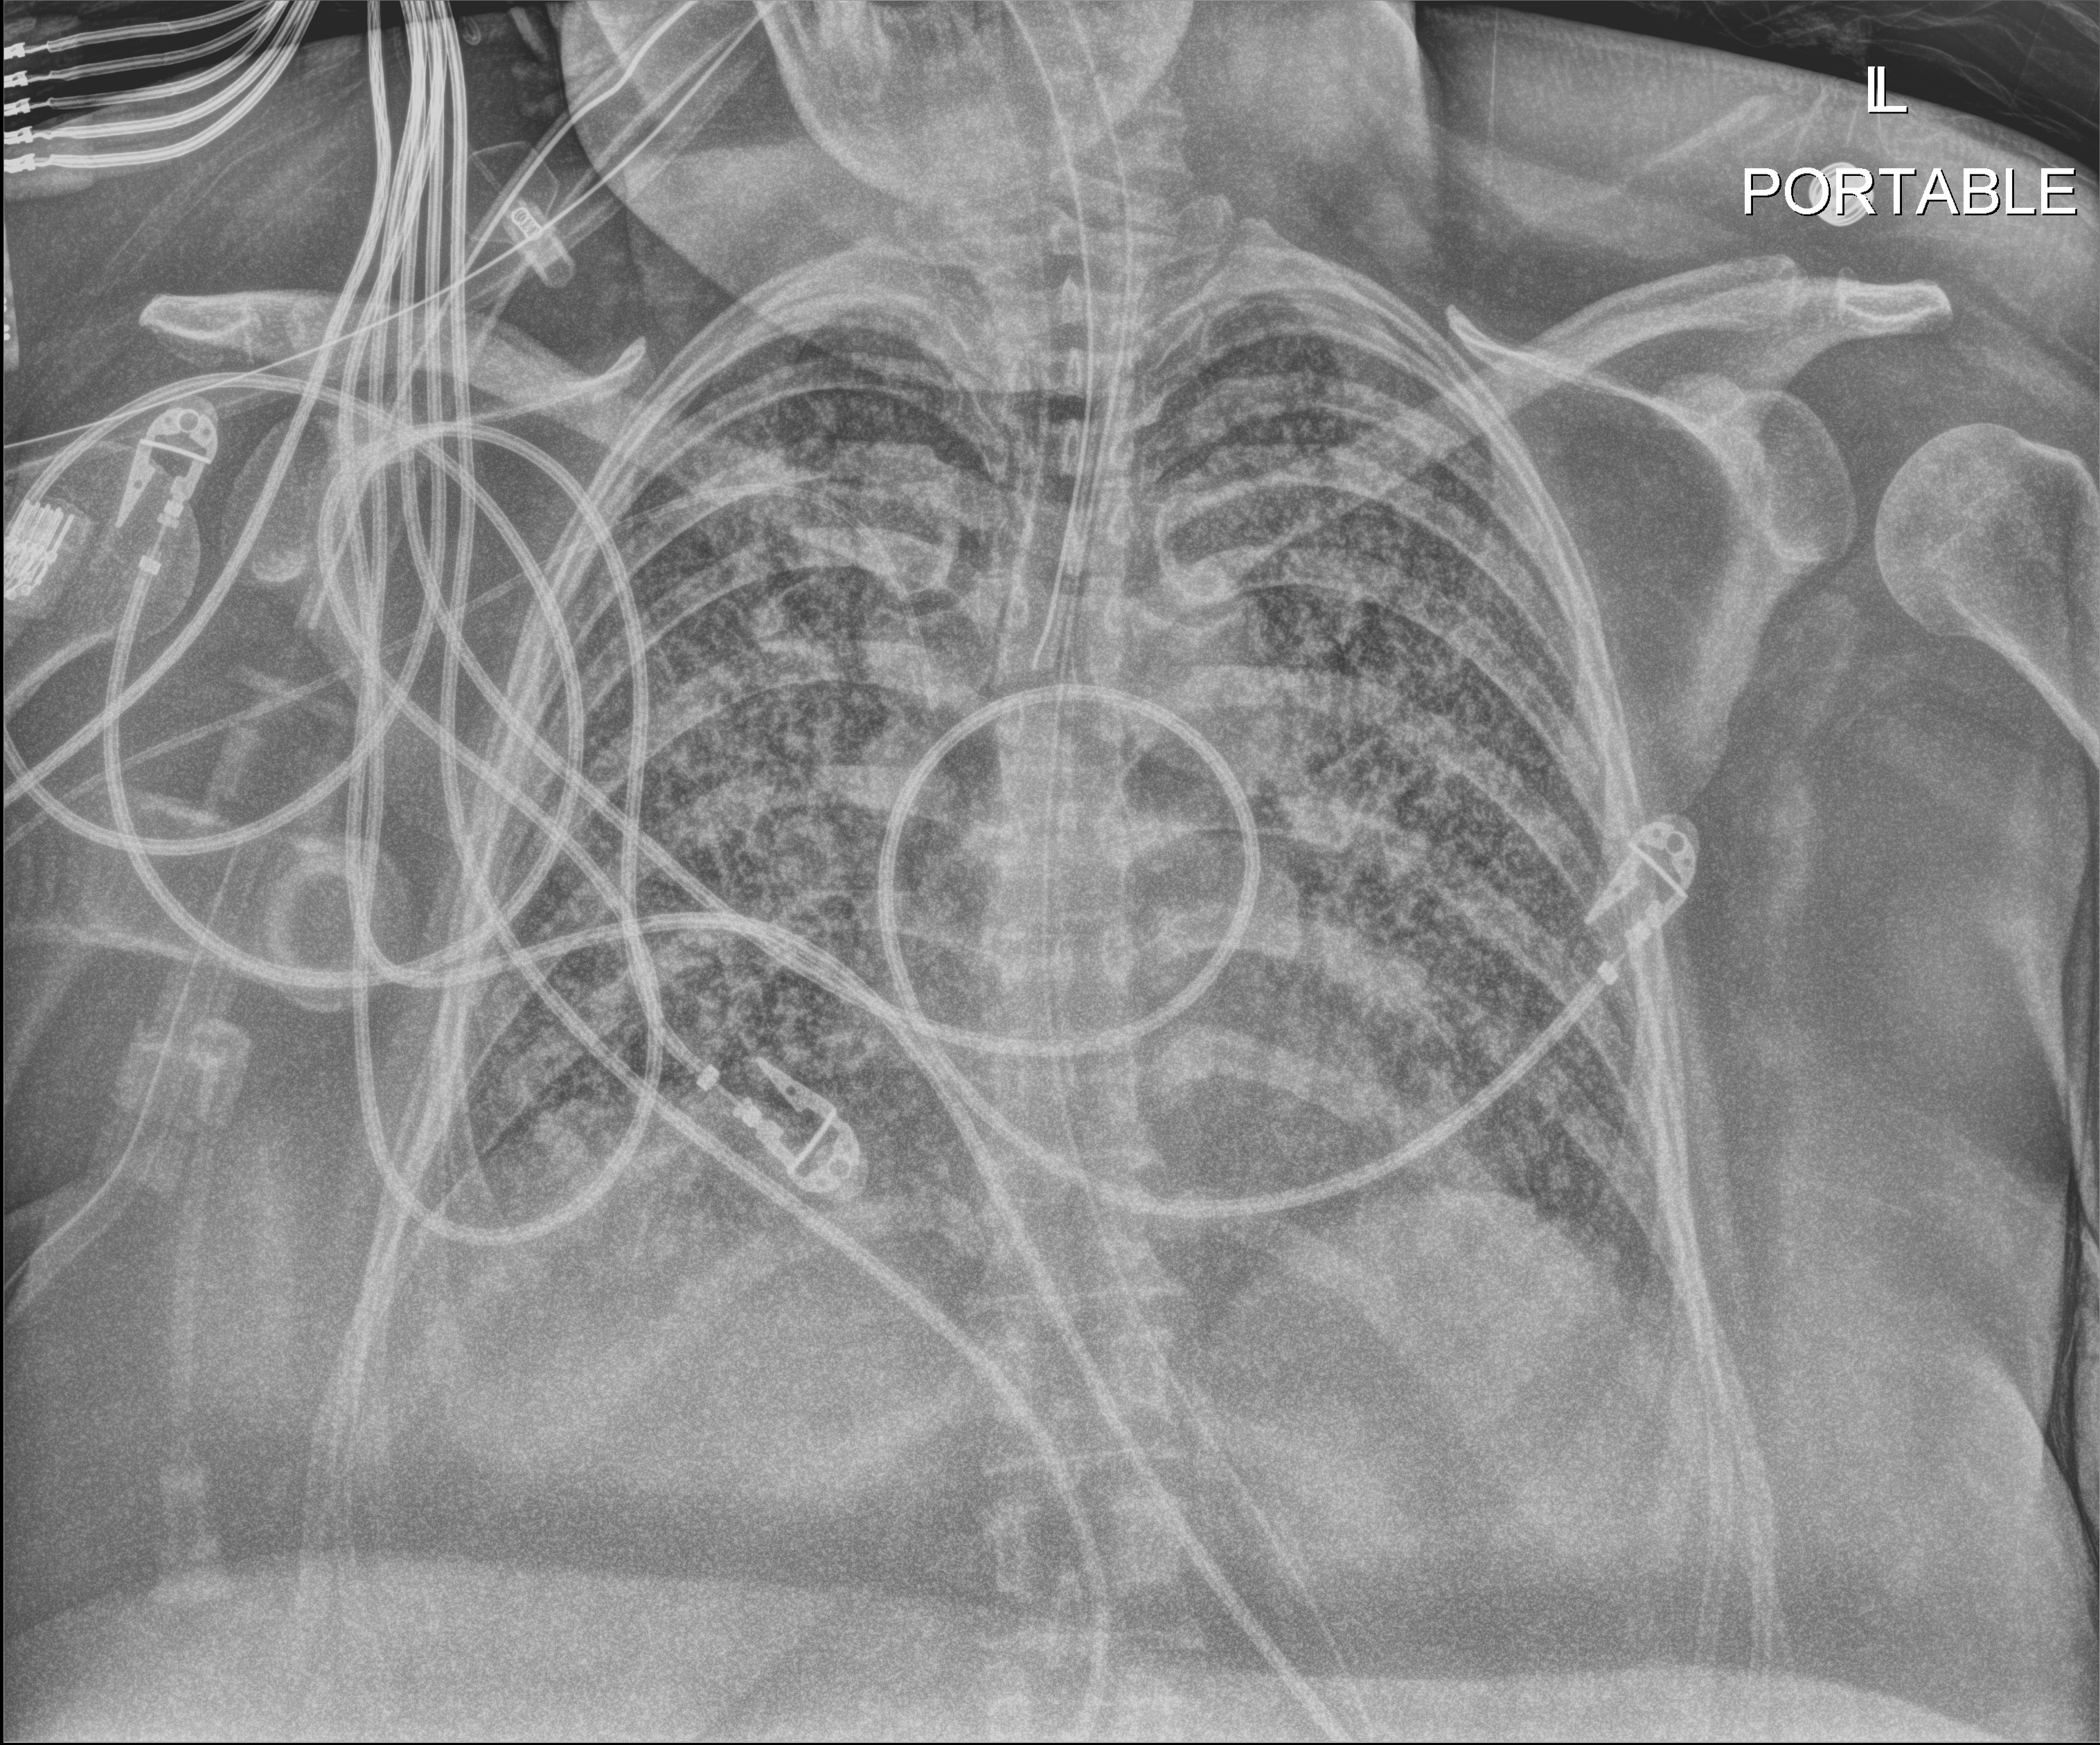
Portable chest radiograph; anteroposterior (AP) projection. Female patient hospitalised with COVID-19, age 18–59 years.
Hospital-stay facts (about this admission, not read from this image; timing relative to this image not recorded): length of hospital stay: 95 days; mechanically ventilated during this hospital stay: yes; admitted to intensive care during this hospital stay: yes.